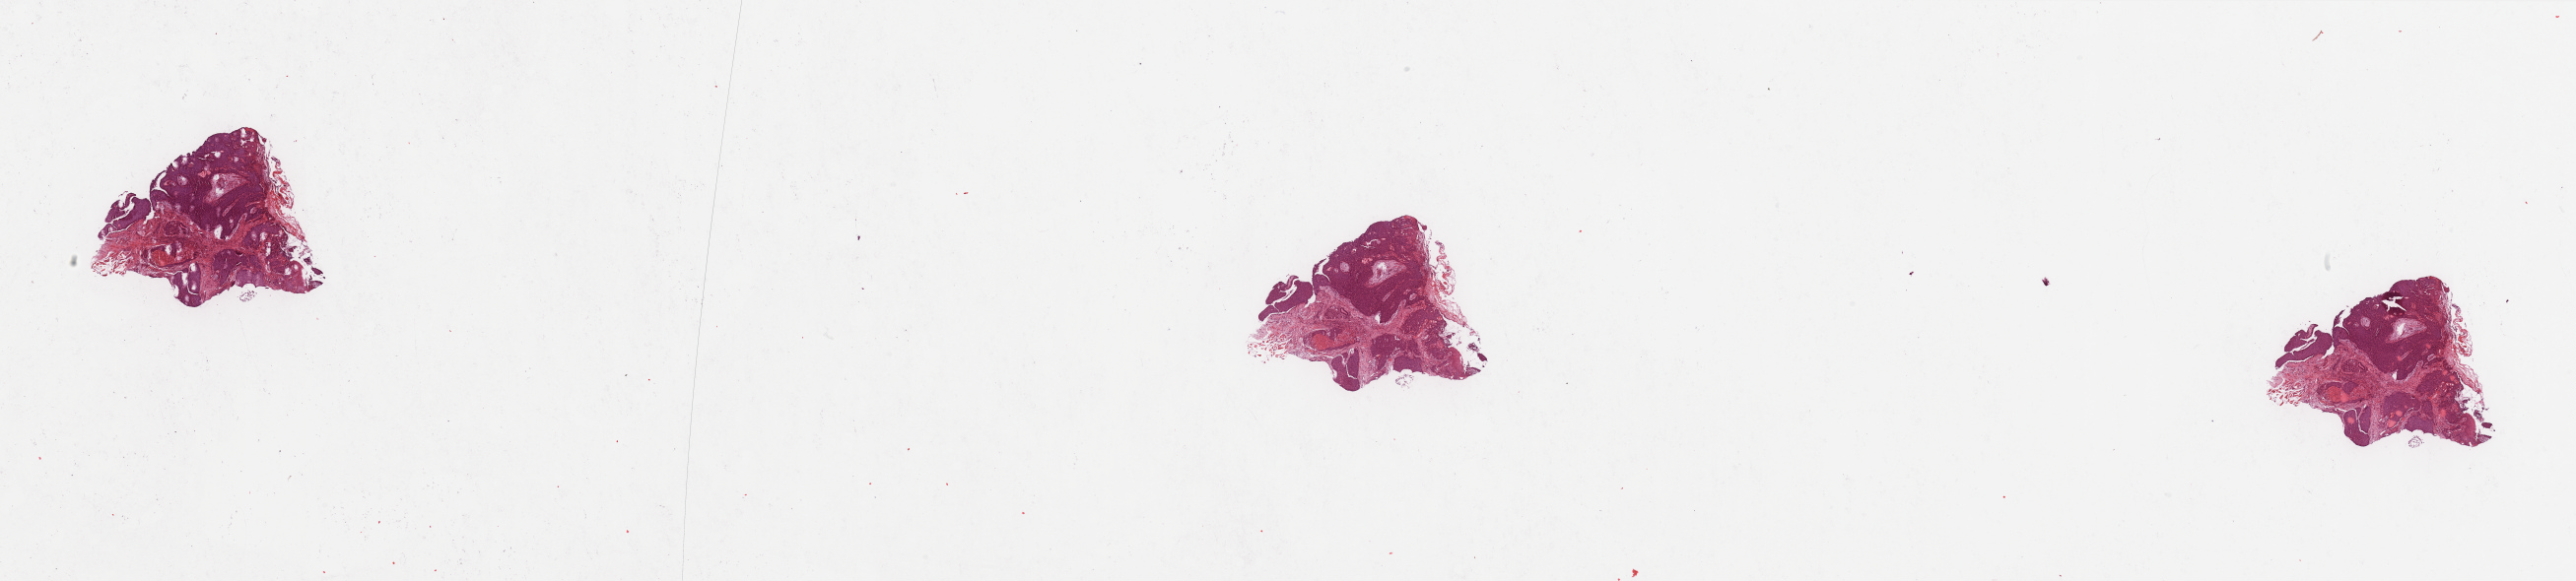
H&E-stained whole-slide image, a low-resolution overview of the entire scanned area, about 41.3 x 9.3 mm (acquisition: 20x scan), tumour tissue sample, sampled site: oropharynx. Patient: male, age 73 years. Histologic grade: G2 (moderately differentiated). Pathologist review of this section (percent, as recorded): tumour nuclei 80%, necrosis 5%.
- histologic diagnosis: Squamous cell carcinoma, NOS (oropharynx, NOS)
- AJCC pathologic stage: II